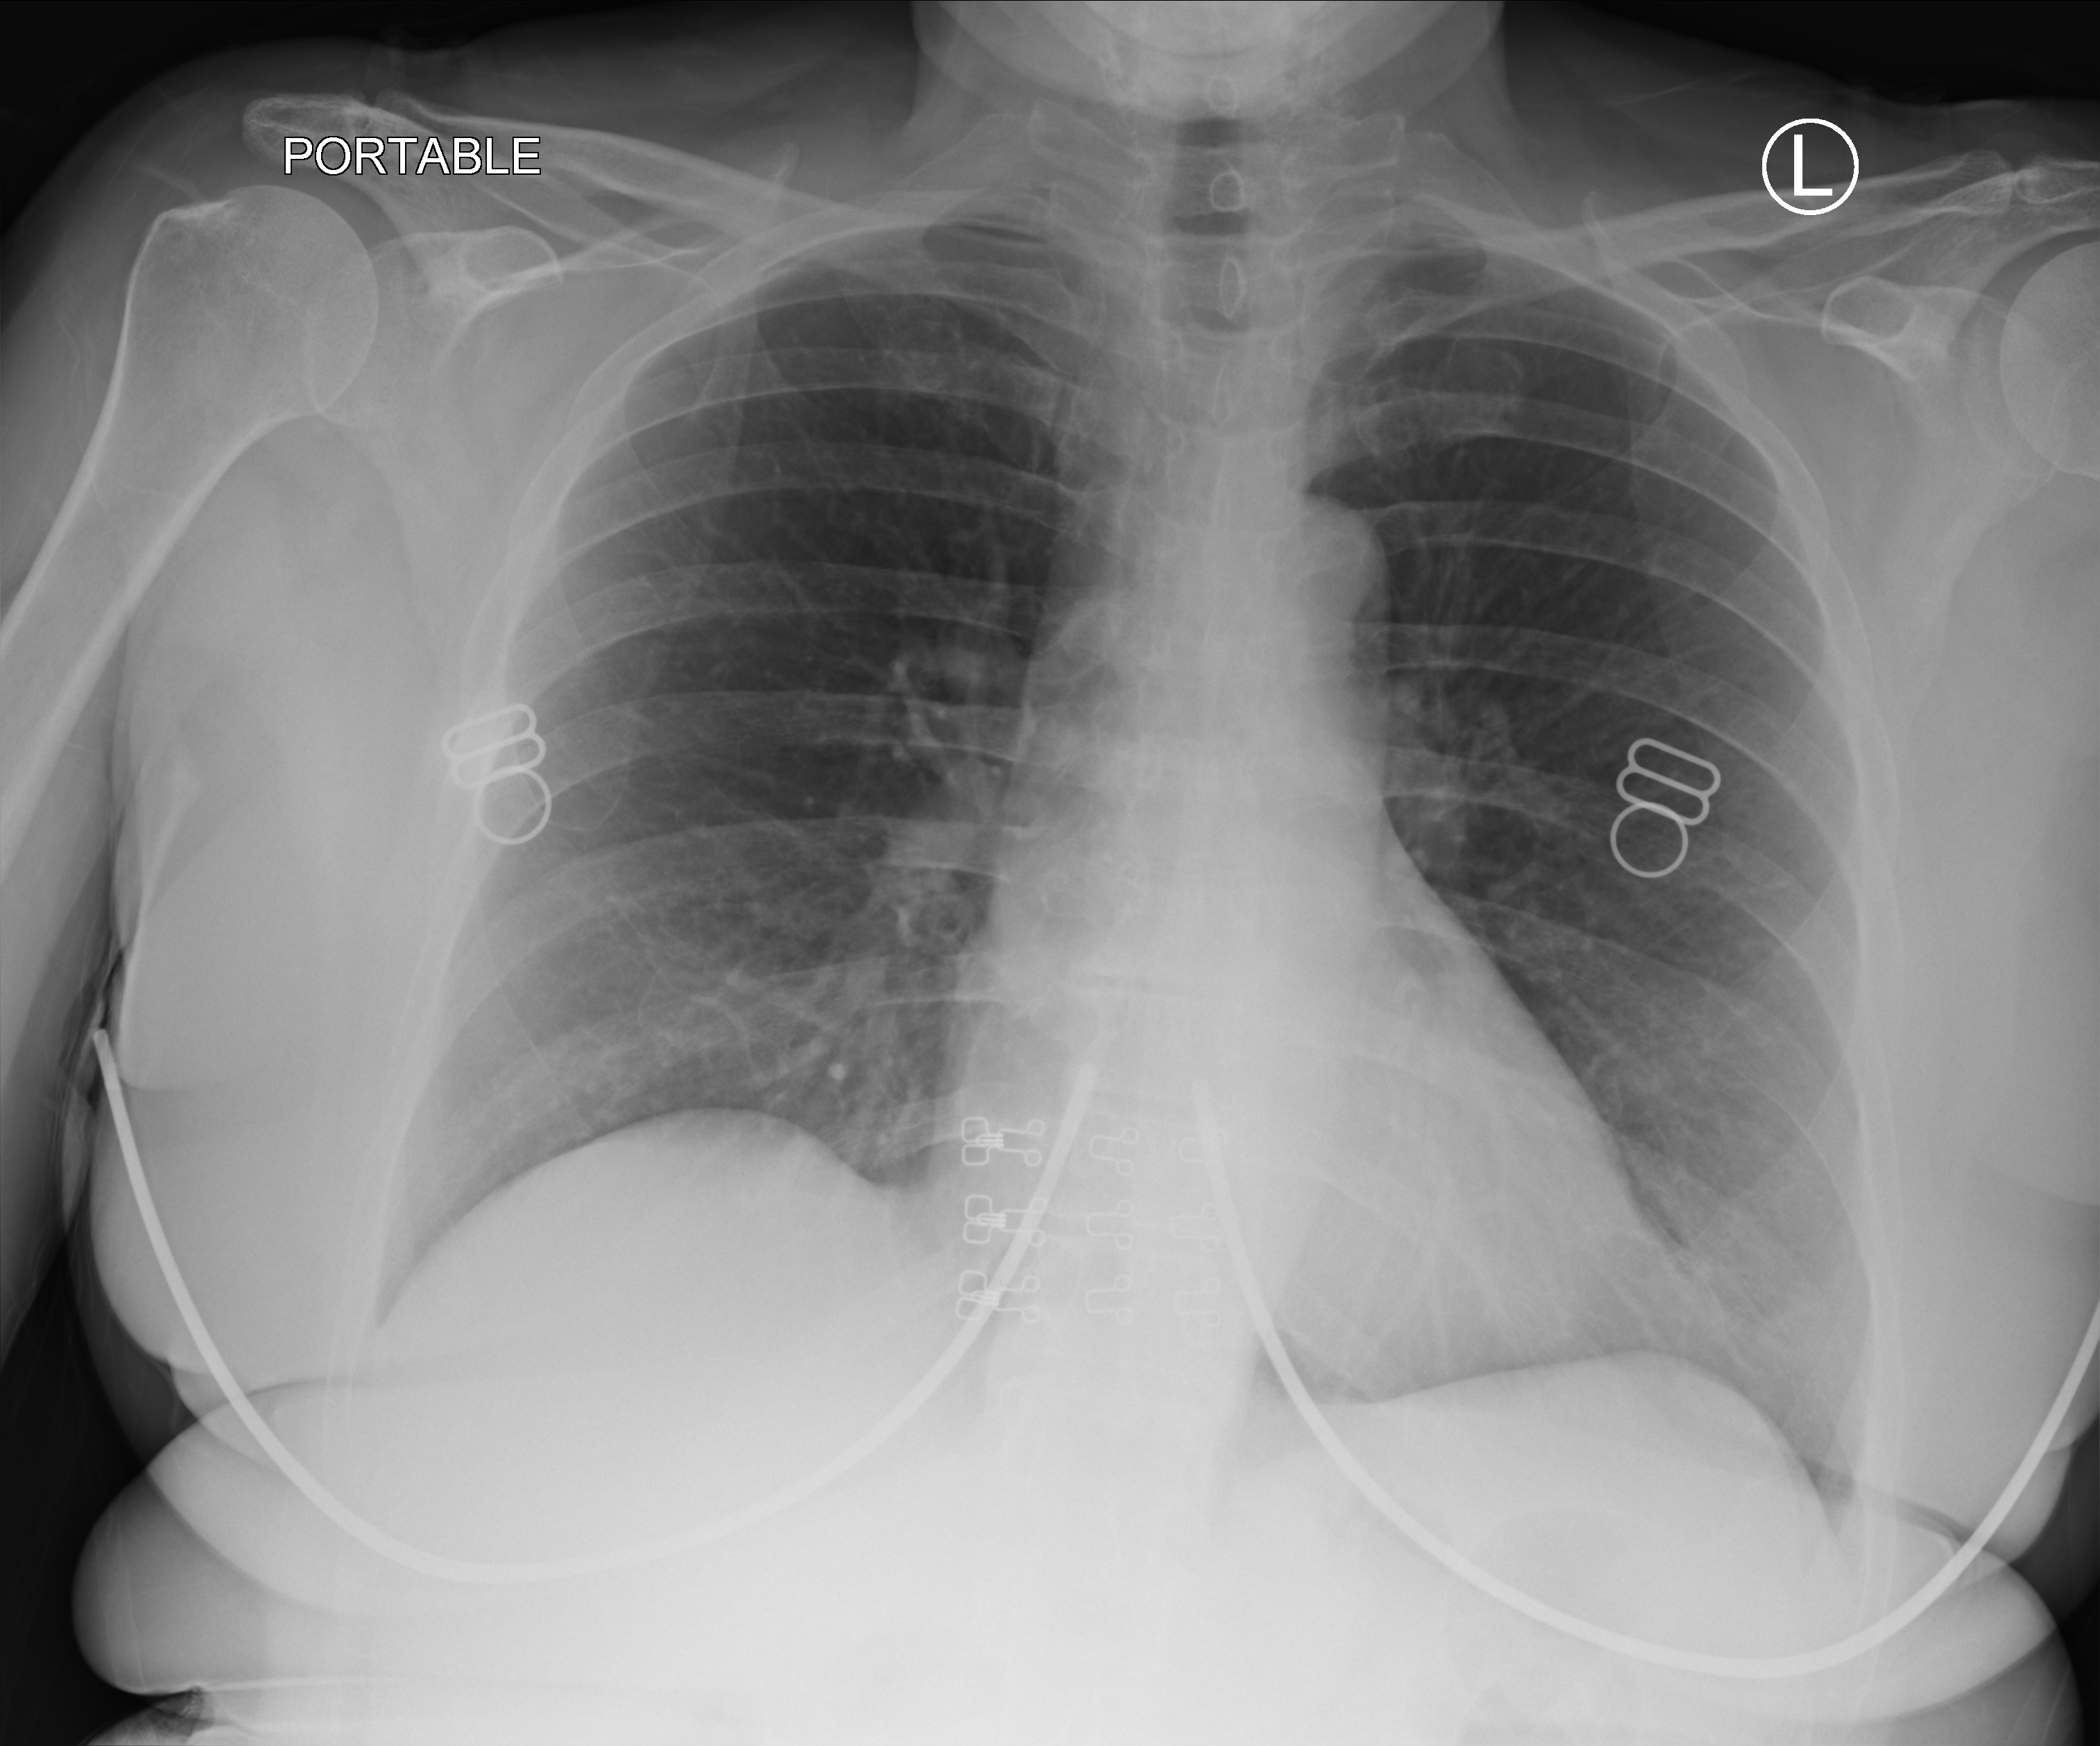
Portable chest radiograph, anteroposterior (AP) projection. Female patient hospitalised with COVID-19, age 18–59 years.
Hospital-stay facts (about this admission, not read from this image; timing relative to this image not recorded):
- COPD (admission record): no
- mechanically ventilated during this hospital stay: no